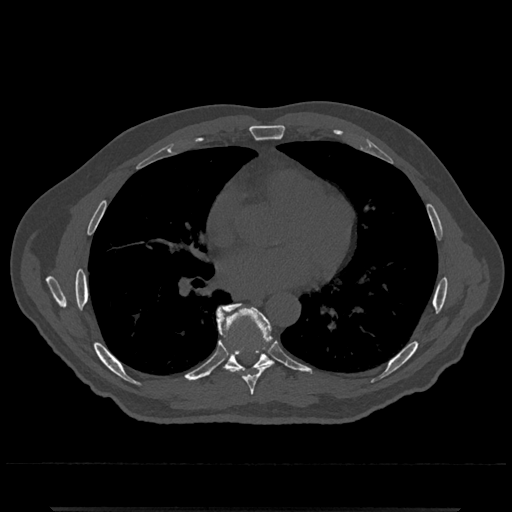
CT including the spine, one axial slice; slice 697 of 797 in the series (ordered by position); 120 kVp; bone window (W 1800 / L 400 HU); 512 × 512 image matrix, field of view 393 × 393 mm. Male patient, age 67 years. Case-level facts recorded for this patient, not image findings: primary cancer: prostate.
Annotated regions visible in this slice (semi-automatic segmentation, software-assisted and operator-edited):
- T7 vertebra: bounding box (x1, y1, x2, y2) in pixels: (218, 310, 272, 395)
- T8 vertebra: (216, 303, 271, 372)